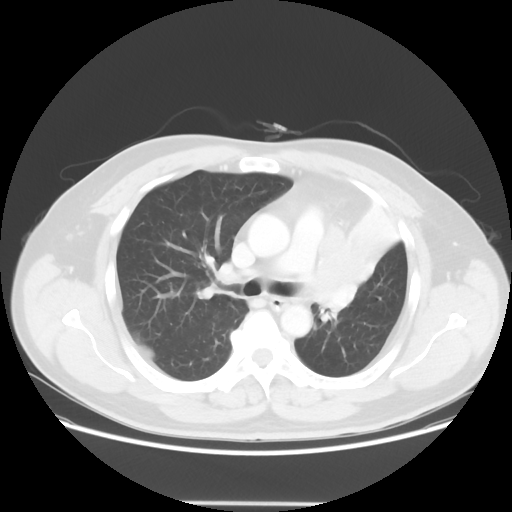
Chest CT, one axial slice; slice 39 of 62 in the series (ordered by position); reconstruction kernel STANDARD; 120 kVp; lung window (W 1500 / L -600 HU); 5 mm slice thickness; 512 × 512 image matrix. Patient: male, 49 years. From the clinical record (not read from this slice): clinical TNM (as recorded): T3 N3 M1c.
Structures marked on this image (rectangle marked by the reading radiologist):
- lung tumour (recorded histology: squamous cell carcinoma): bounding box <317,226,381,325> (left, top, right, bottom; pixels)